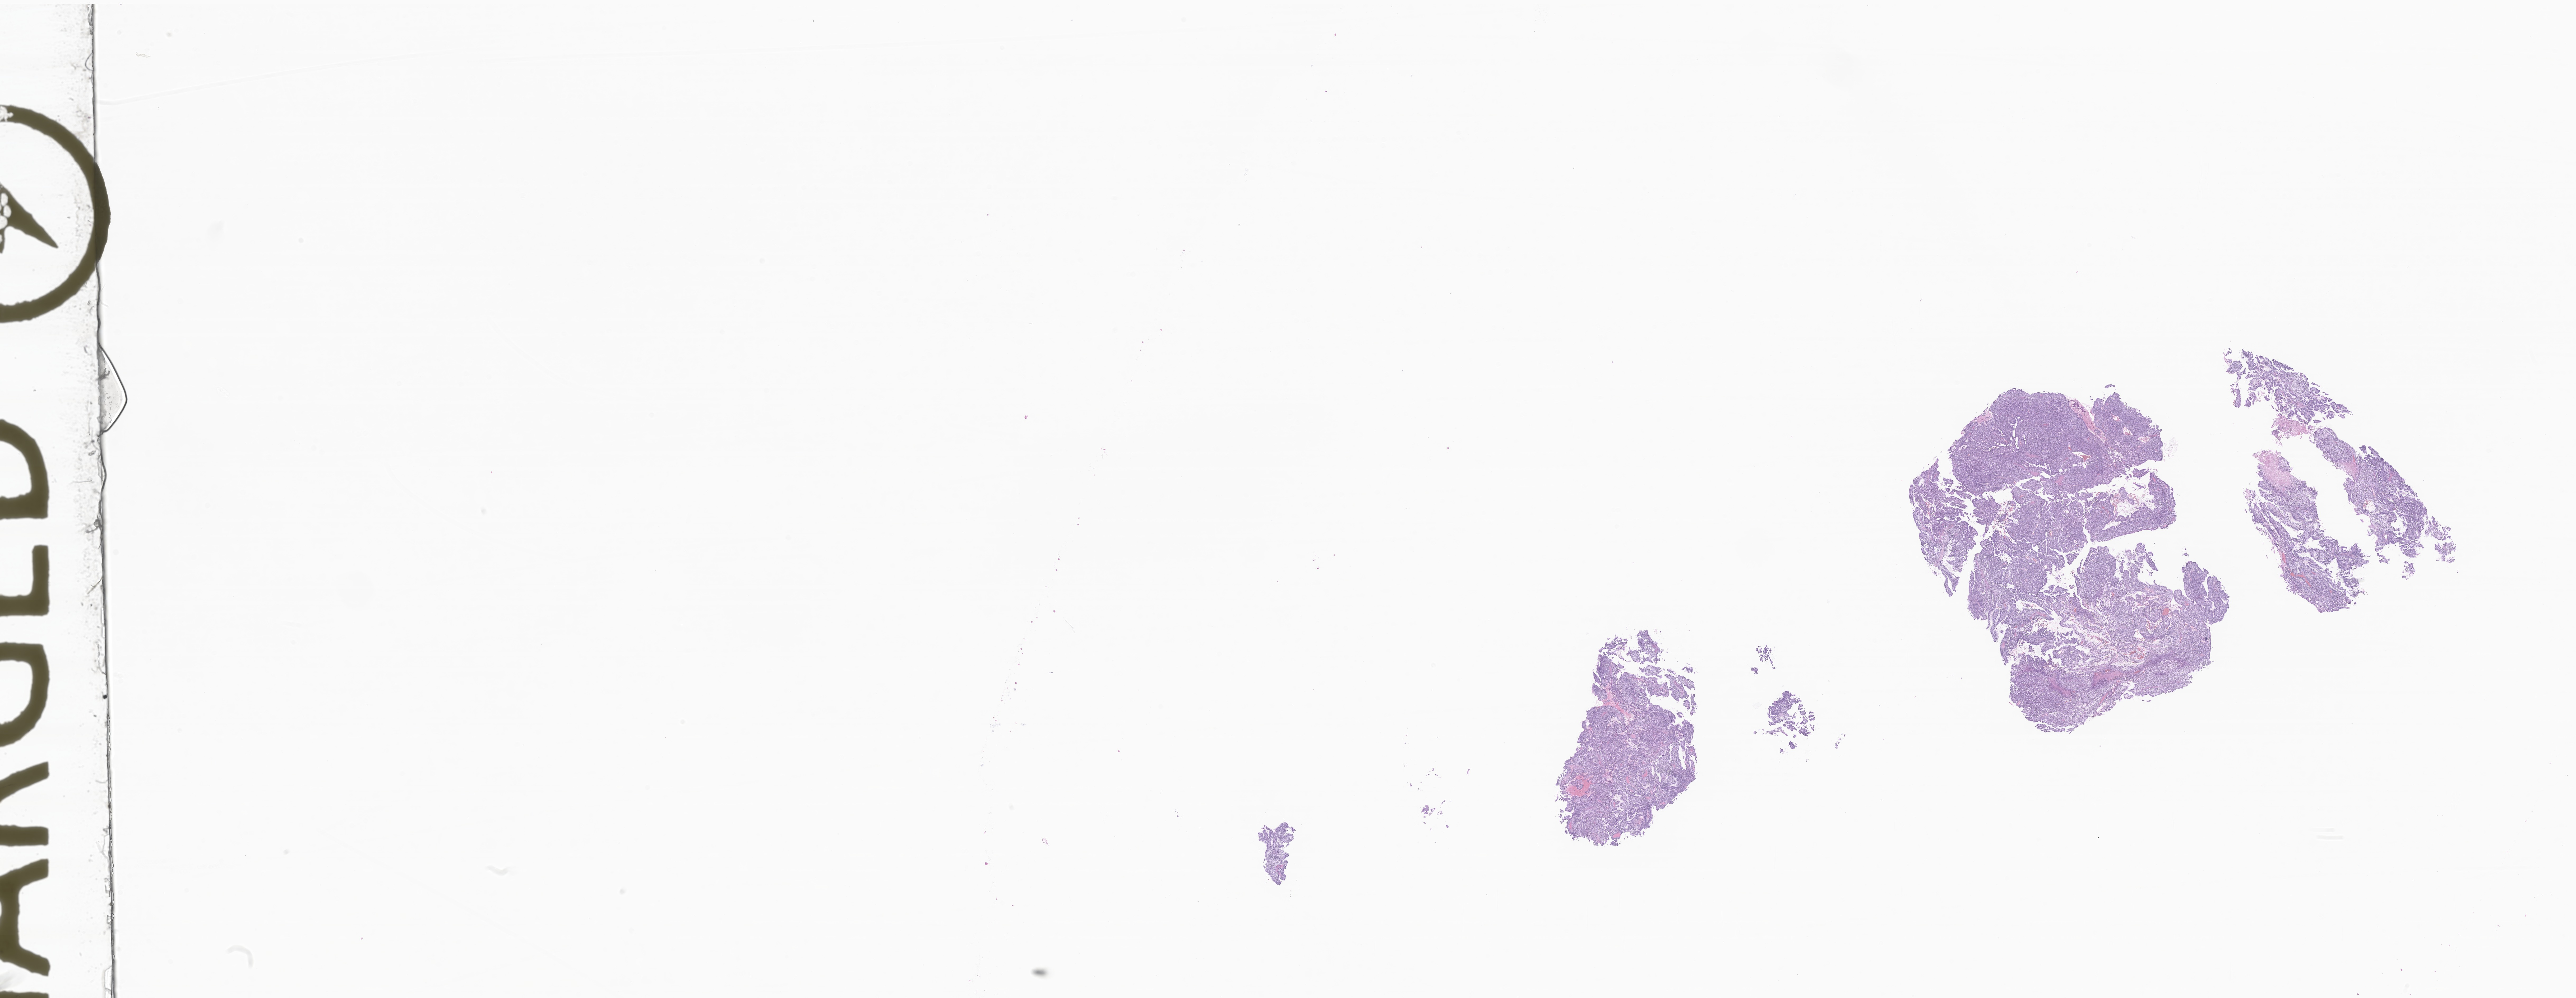
Whole-slide image, H&E stain of tumor tissue from the cerebral ventricle — shown as a low-resolution overview of the whole scanned area (about 41.1 x 15.9 mm), formalin-fixed paraffin-embedded section. Patient female; age 109 days.
* diagnosis: Choroid plexus carcinoma